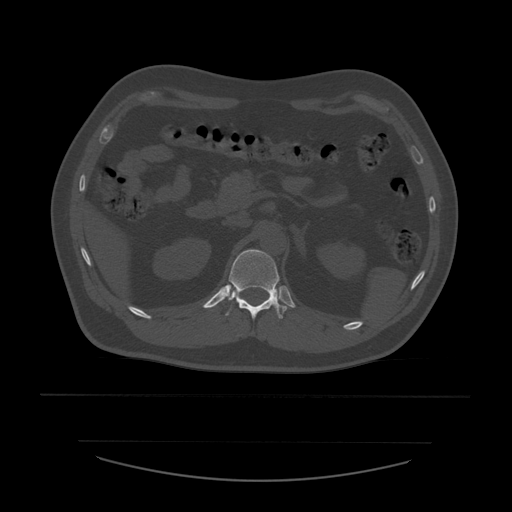
CT including the spine, one axial slice. Slice 249 of 532 in the series (ordered by position). Reconstruction kernel STANDARD. 120 kVp. Bone window (W 1800 / L 400 HU). 1.25 mm slice thickness. 512 × 512 image matrix, field of view 441 × 441 mm. Patient age 44 years. From the clinical record (not read from this slice): primary cancer: soft tissue sarcoma.
Annotated regions visible in this slice (semi-automatic segmentation, software-assisted and operator-edited):
- T12 vertebra: bounding box [x1, y1, x2, y2] px = [225, 250, 288, 319]